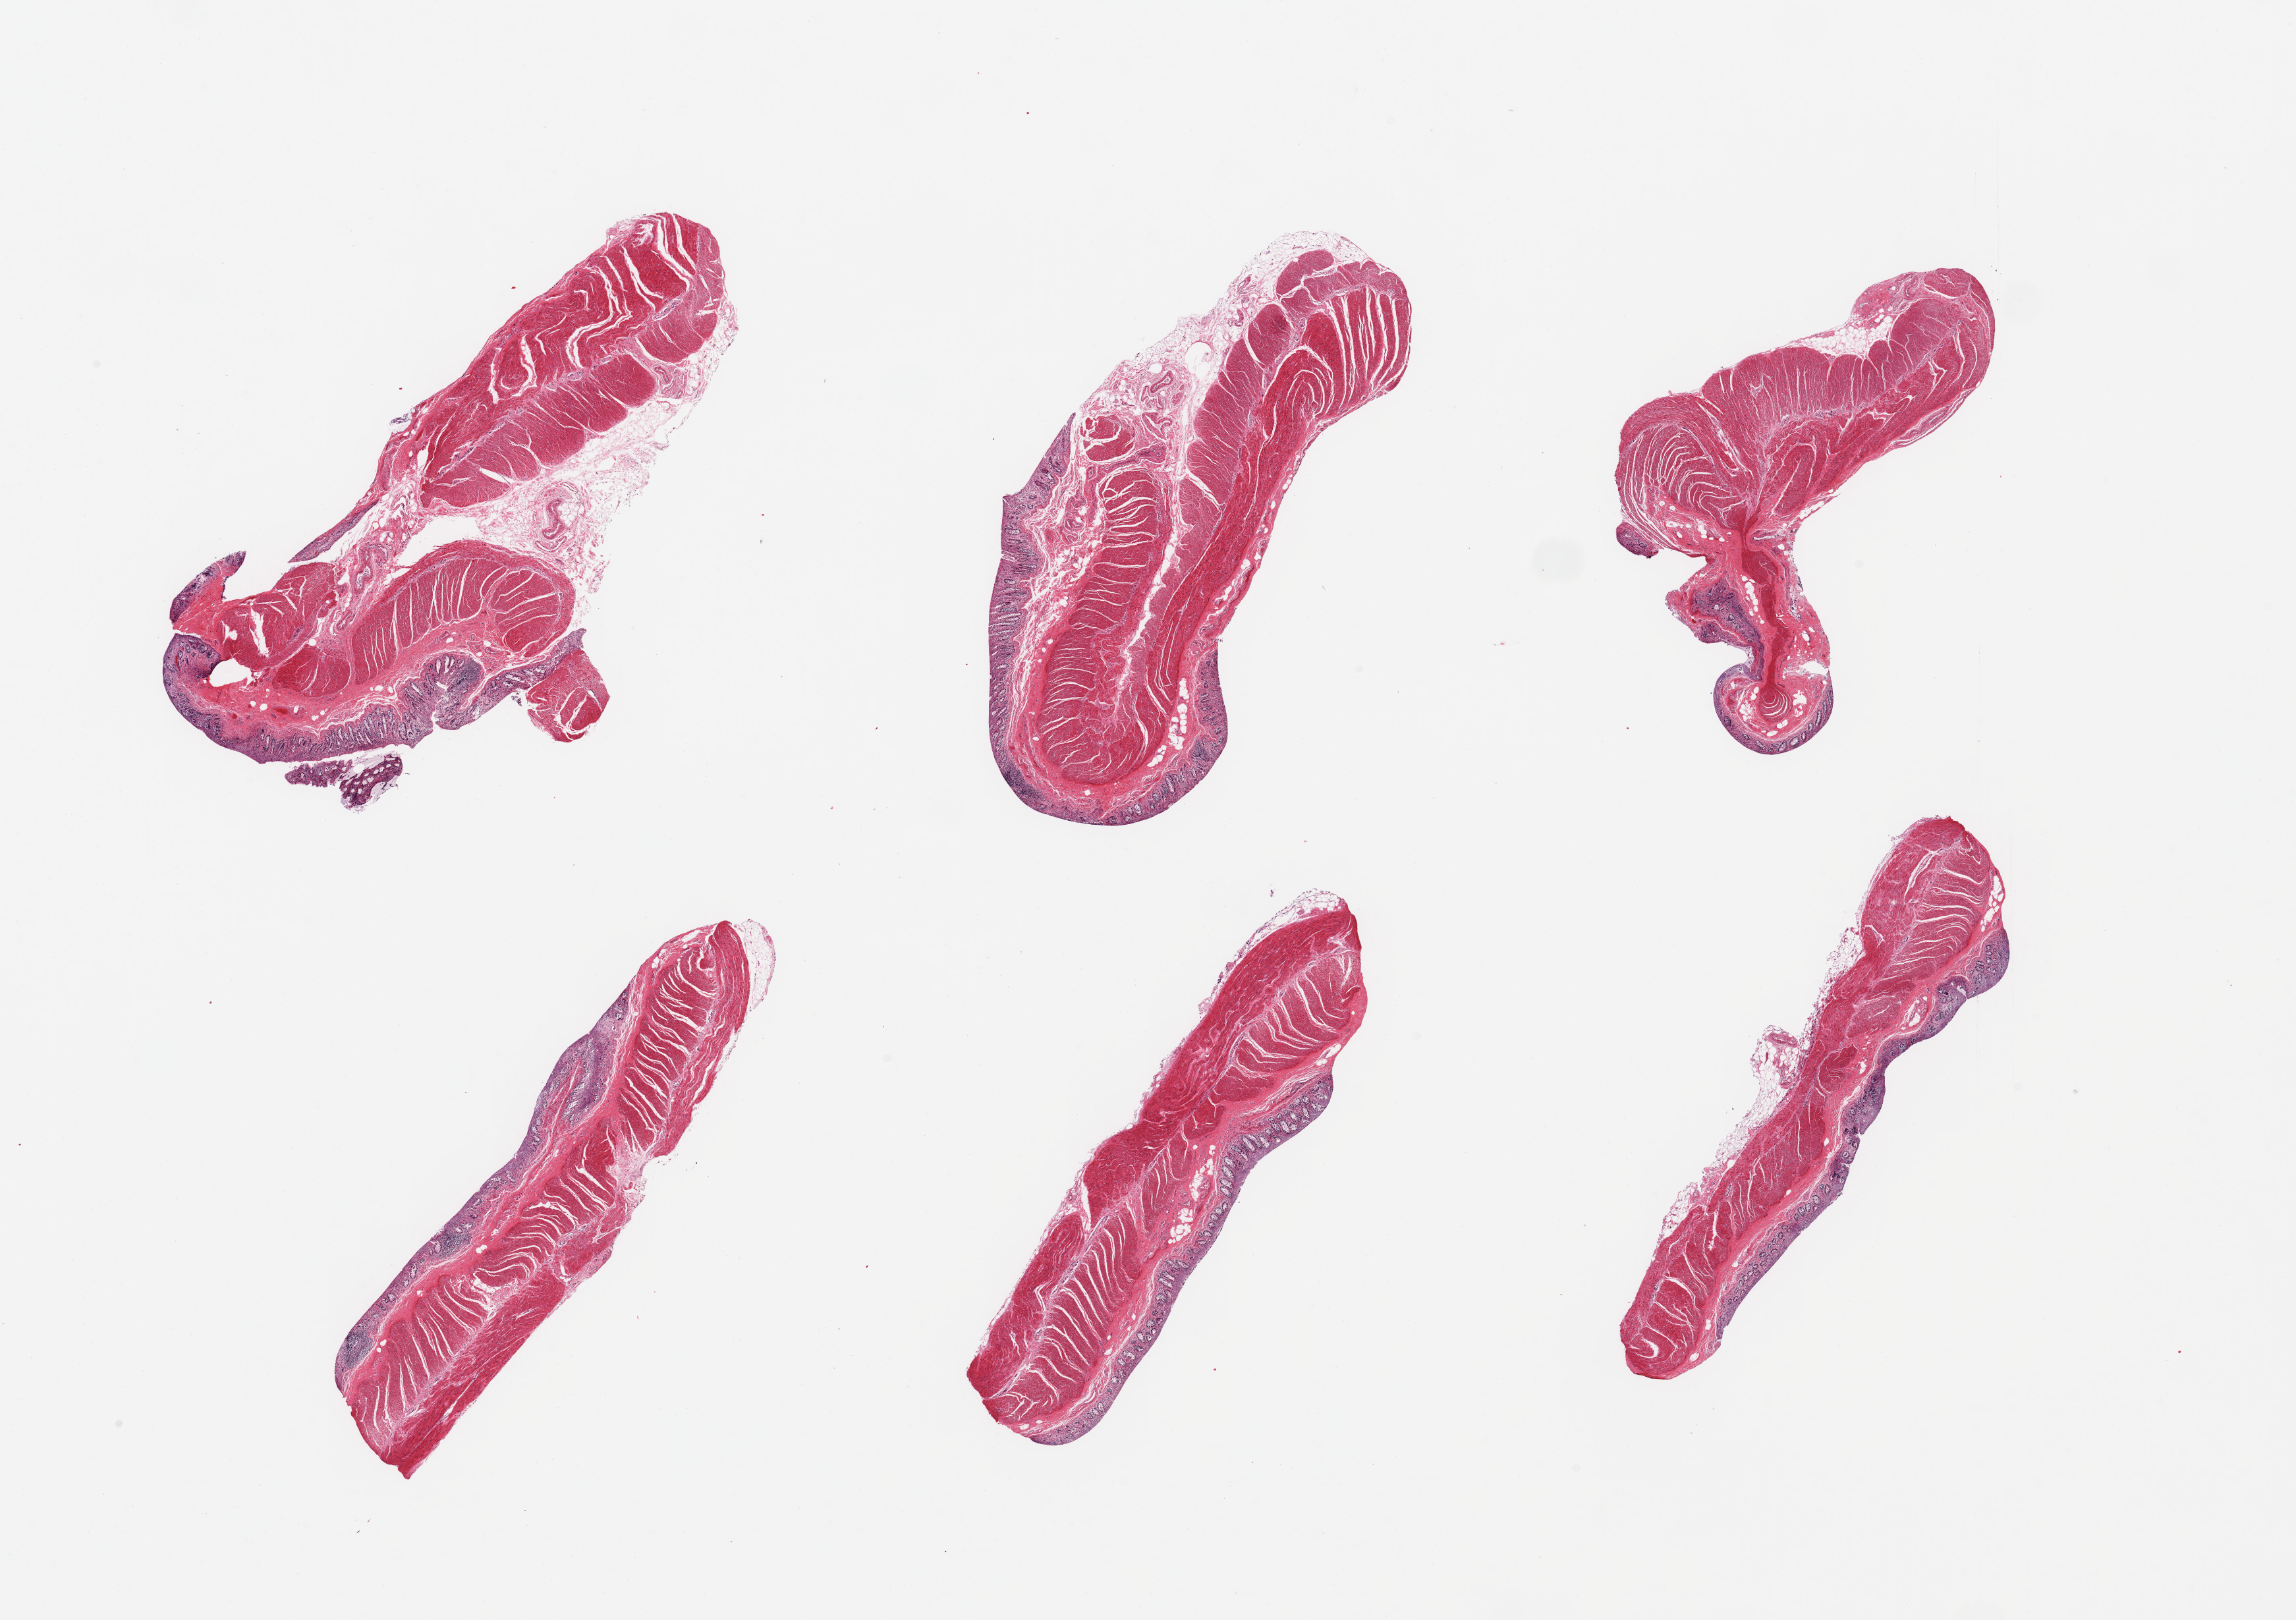
Digitized haematoxylin and eosin-stained section — low-resolution overview of the scanned area, about 27.6 x 19.4 mm (slide scanned at 20x). PAXgene-fixed, paraffin-embedded tissue. Sampled site (target tissue): transverse colon. Donor tissue sample. Donor: male.
Reviewer comment on this tissue sample: 6 pieces, target mucosa up to ~0.35mm, advanced autolysis.